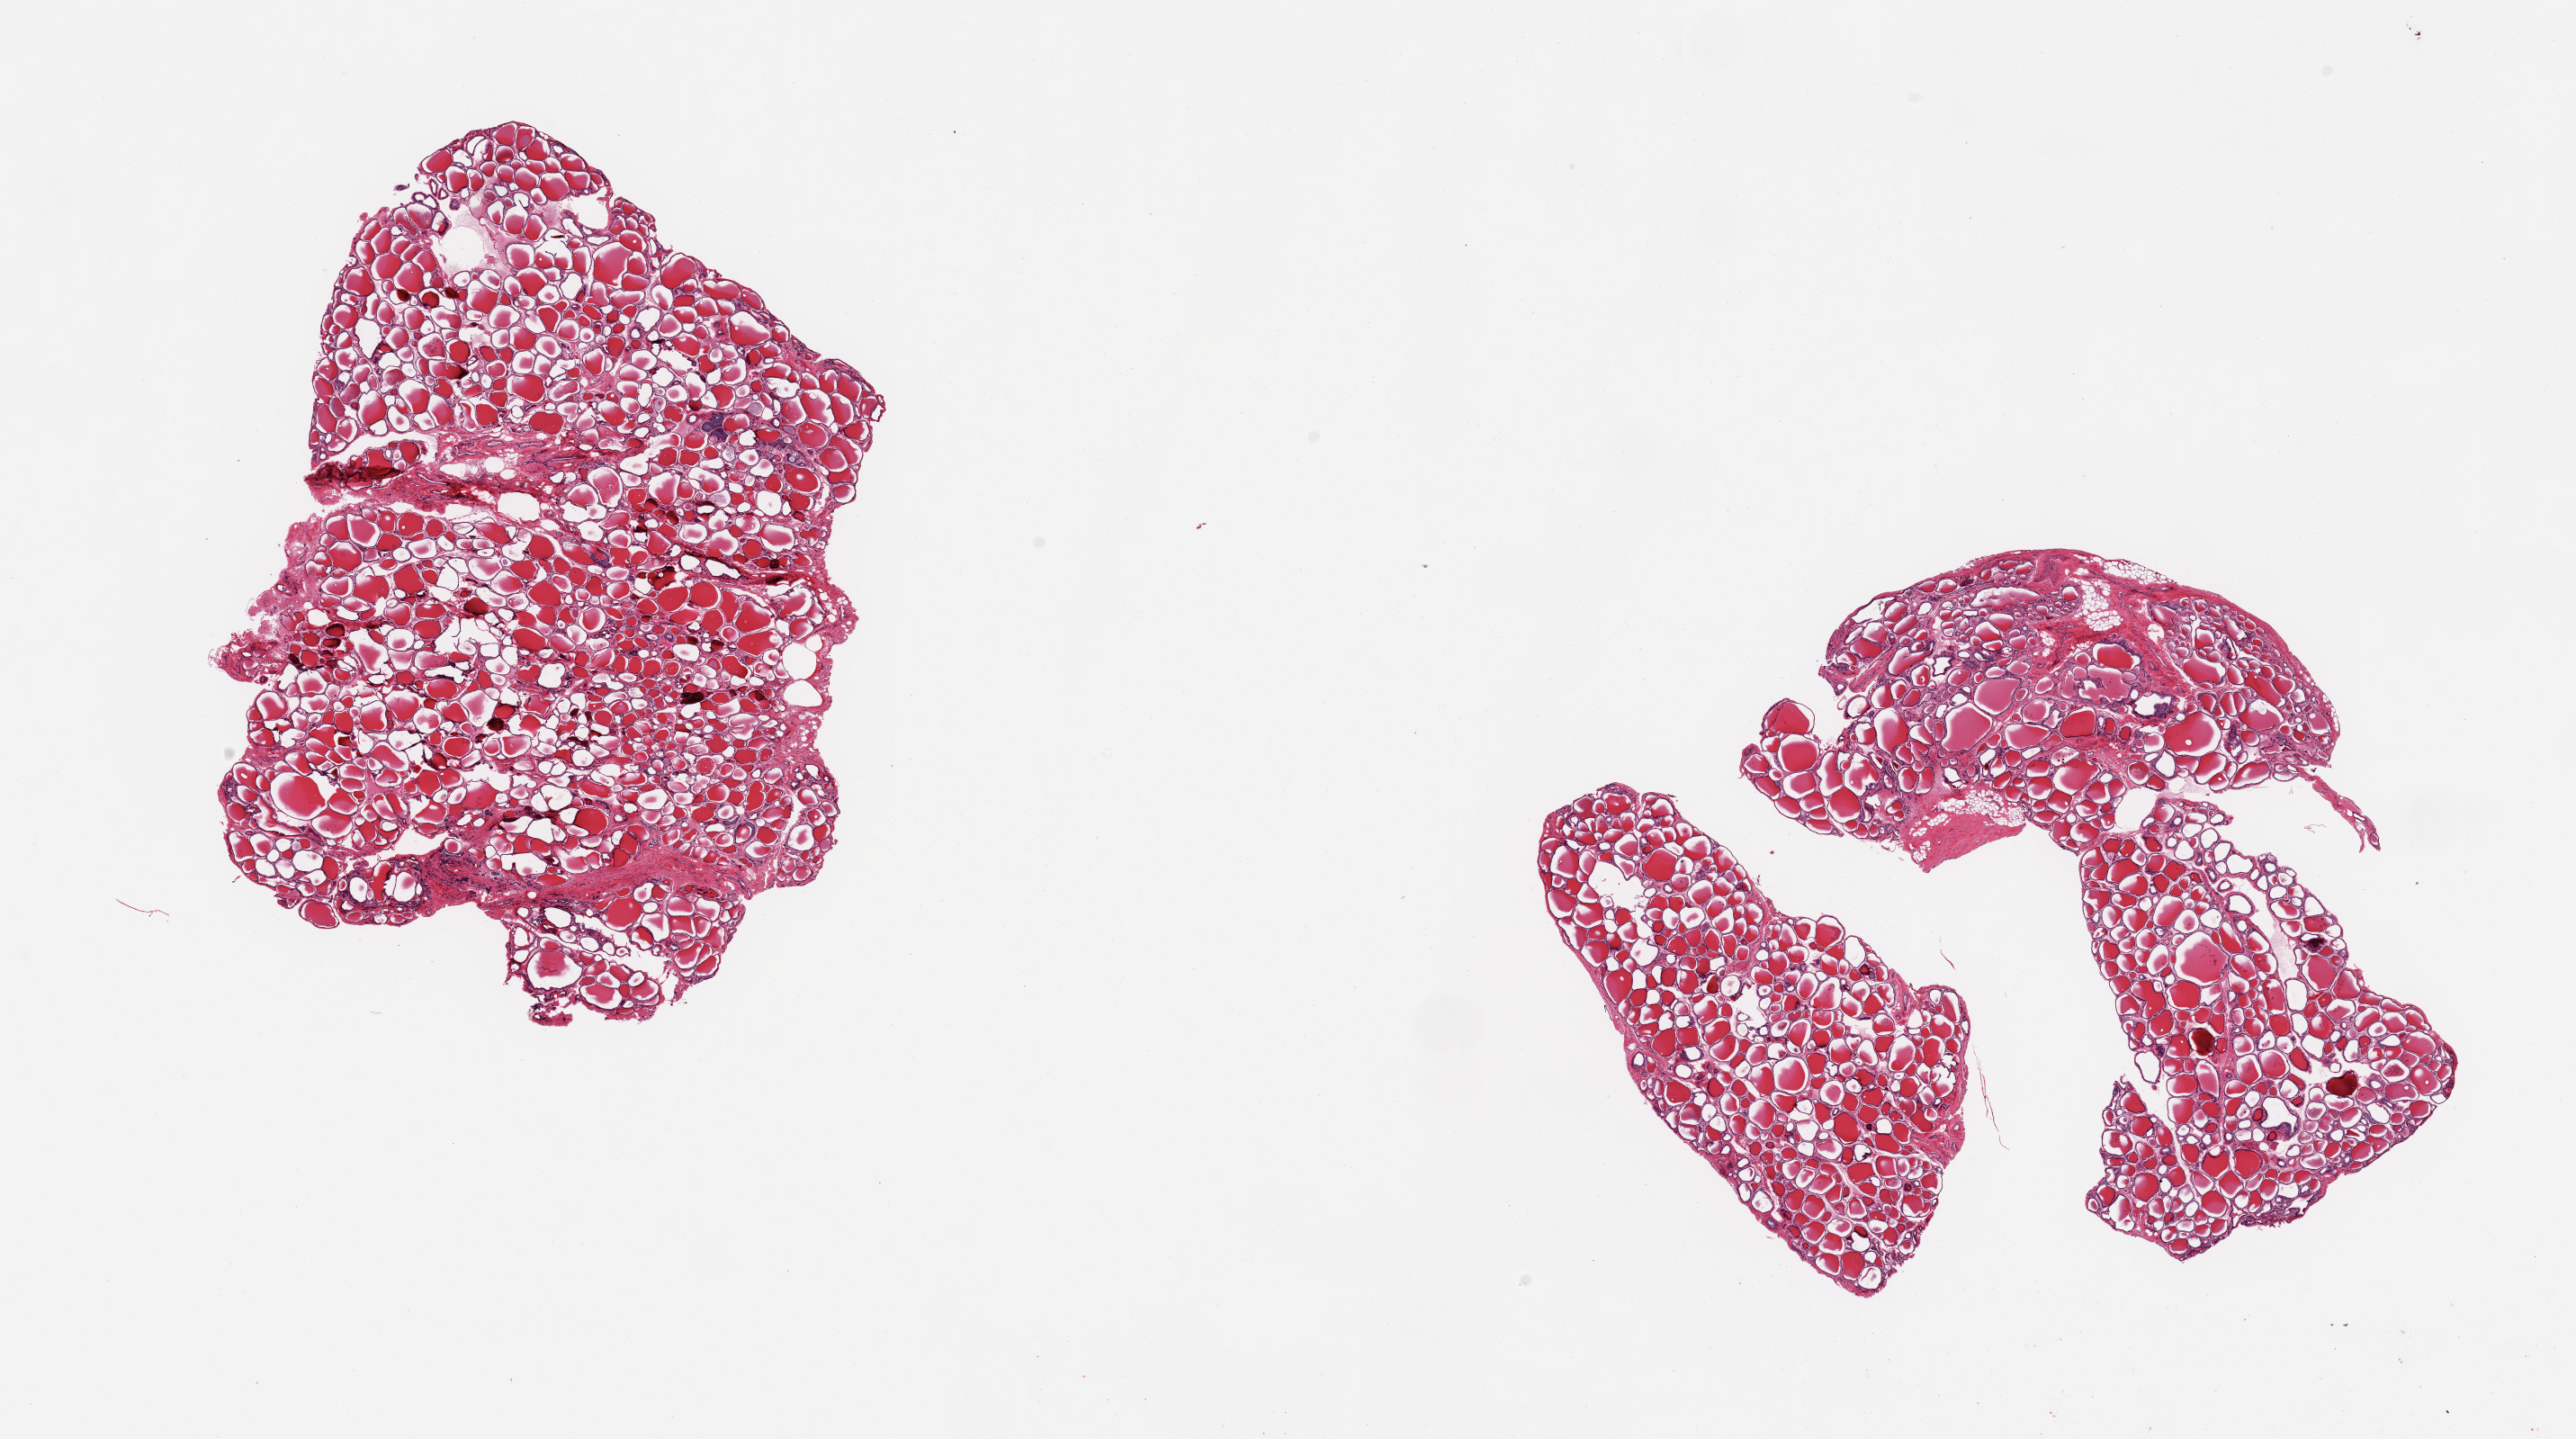
Whole-slide image, hematoxylin and eosin (H&E) stain, whole scanned area (about 22.6 x 12.6 mm, acquisition: 20x scan) shown as a low-resolution overview; PAXgene-fixed, paraffin-embedded tissue; sampled site (target tissue): thyroid; donor tissue sample. Donor: male.
- review note (as recorded): 2 pieces; well dissected; no extraneous tissue